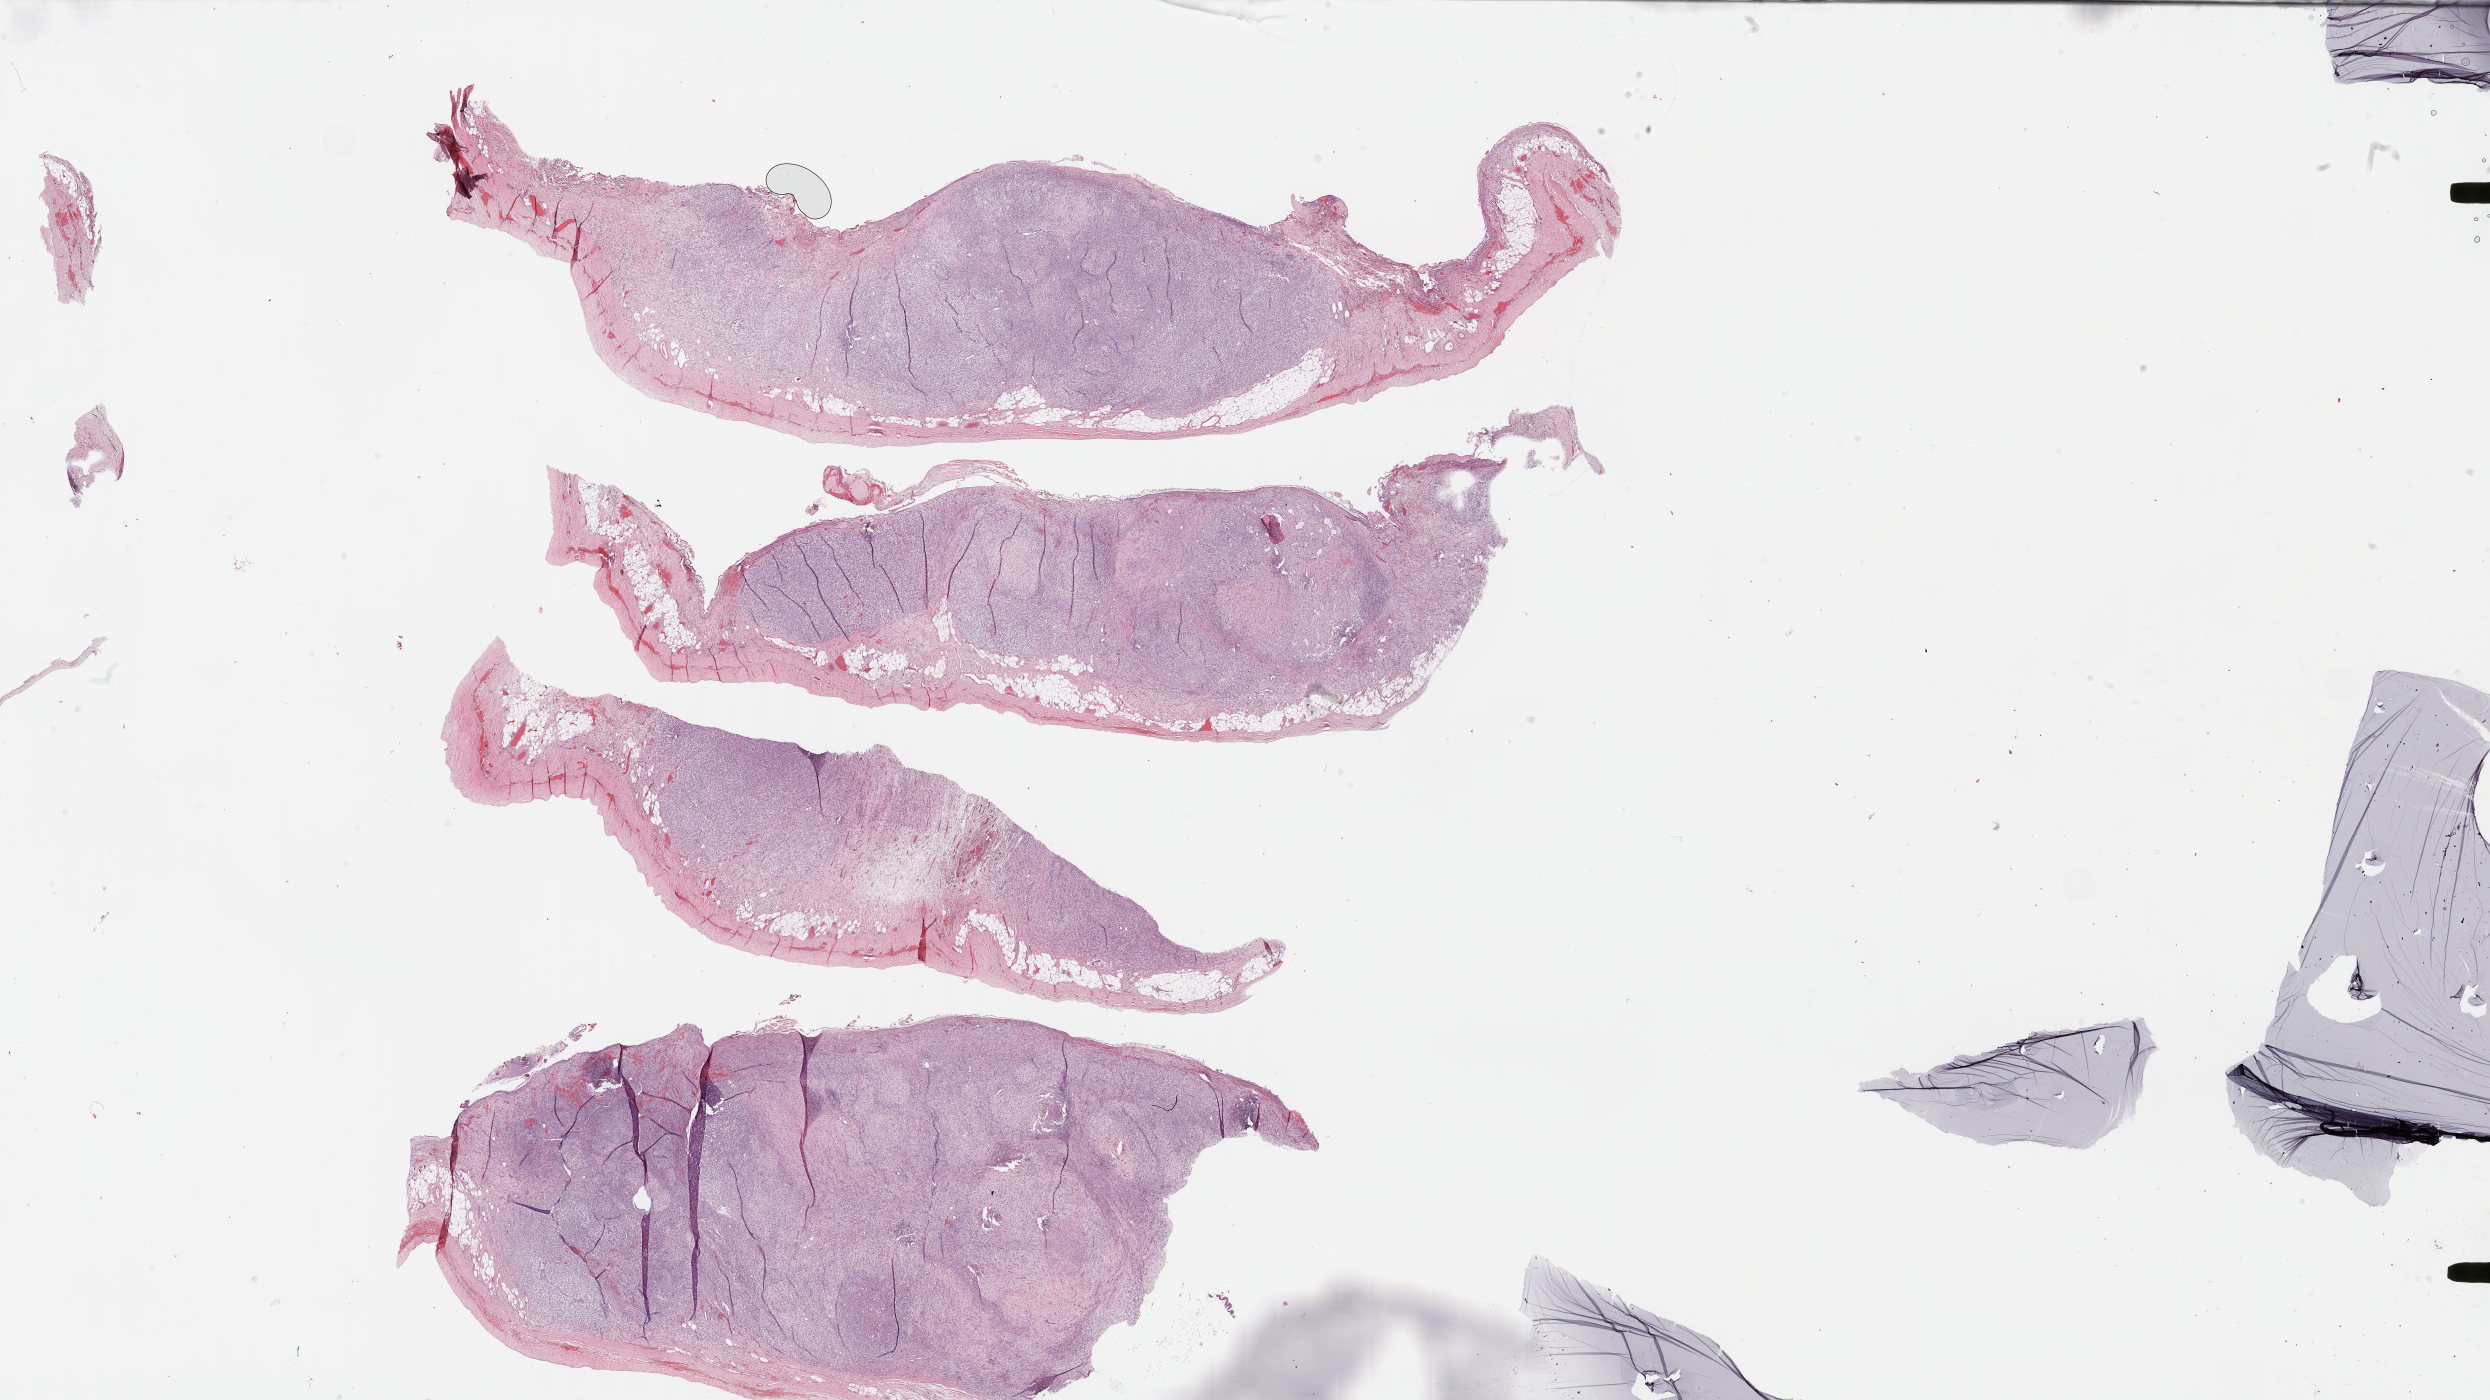
Whole-slide histology image, H&E-stained, low-resolution overview of the scanned area, about 40.2 x 22.6 mm. FFPE section. Primary tumour sample from the mesothelium. Patient: male, age at initial diagnosis 62 years.
• AJCC pathologic stage: III (7th edition)
• TNM: T3 N2 MX
• pathologic diagnosis: Epithelioid mesothelioma, malignant (pleura, NOS)